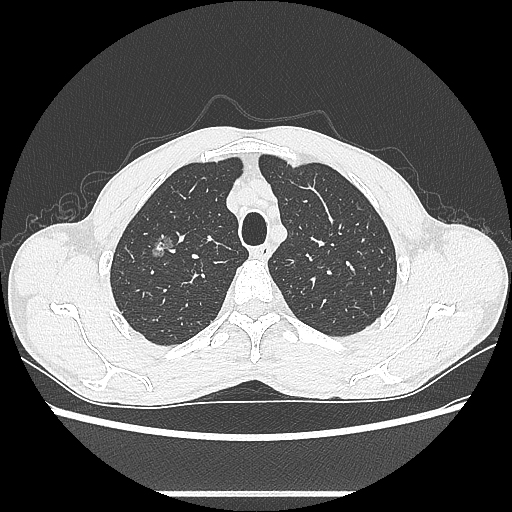
Chest CT, one axial slice; position 482 of 601 along the scan axis; reconstruction kernel LUNG; lung window (W 1500 / L -600 HU); 512 × 512 image matrix, field of view 357 × 357 mm. Patient: male, 54 years. From the clinical record (not read from this slice): clinical TNM (as recorded): T1a N0 M0.
Outlined on this slice (rectangle marked by the reading radiologist):
- lung tumour (recorded histology: adenocarcinoma): box from (x=142, y=228) to (x=177, y=260) px